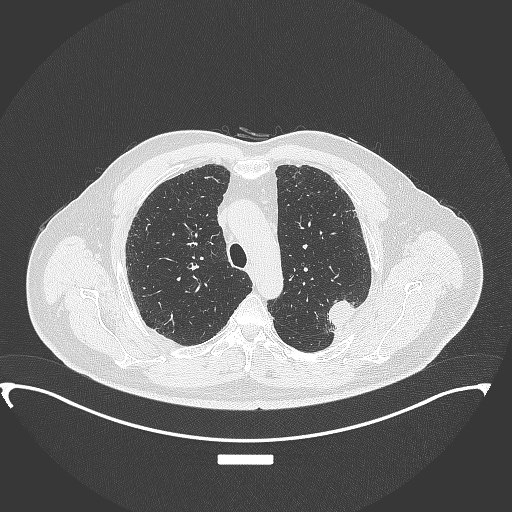
Chest CT, one axial slice; slice 269 of 350 in the series (ordered by position); 120 kVp; lung window (W 1500 / L -600 HU); 1 mm slice thickness; 512 × 512 image matrix, field of view 459 × 459 mm. Patient: male, 64 years. Case-level facts recorded for this patient, not image findings: clinical TNM (as recorded): T1c N1 M1.
Outlined on this slice (bounding box drawn by a radiologist):
- lung tumour (recorded histology: adenocarcinoma): bounding box <327,295,364,342> (left, top, right, bottom; pixels)